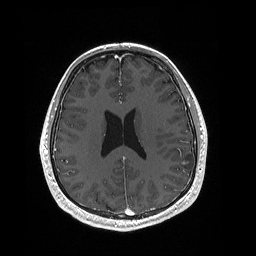
Brain MRI from a brain-tumour surgery series, one axial slice. Position 83 of 192 along the scan axis. T1-weighted post-contrast. 1 mm slice thickness. 256 × 256 image matrix. From the clinical record (not read from this slice): histopathology: Dysembryoplastic neuroepithelial tumor; WHO grade: 1; IDH mutation: no.
Structures marked on this image (expert manual segmentation):
- tumour: box from (x=180, y=159) to (x=190, y=166) px